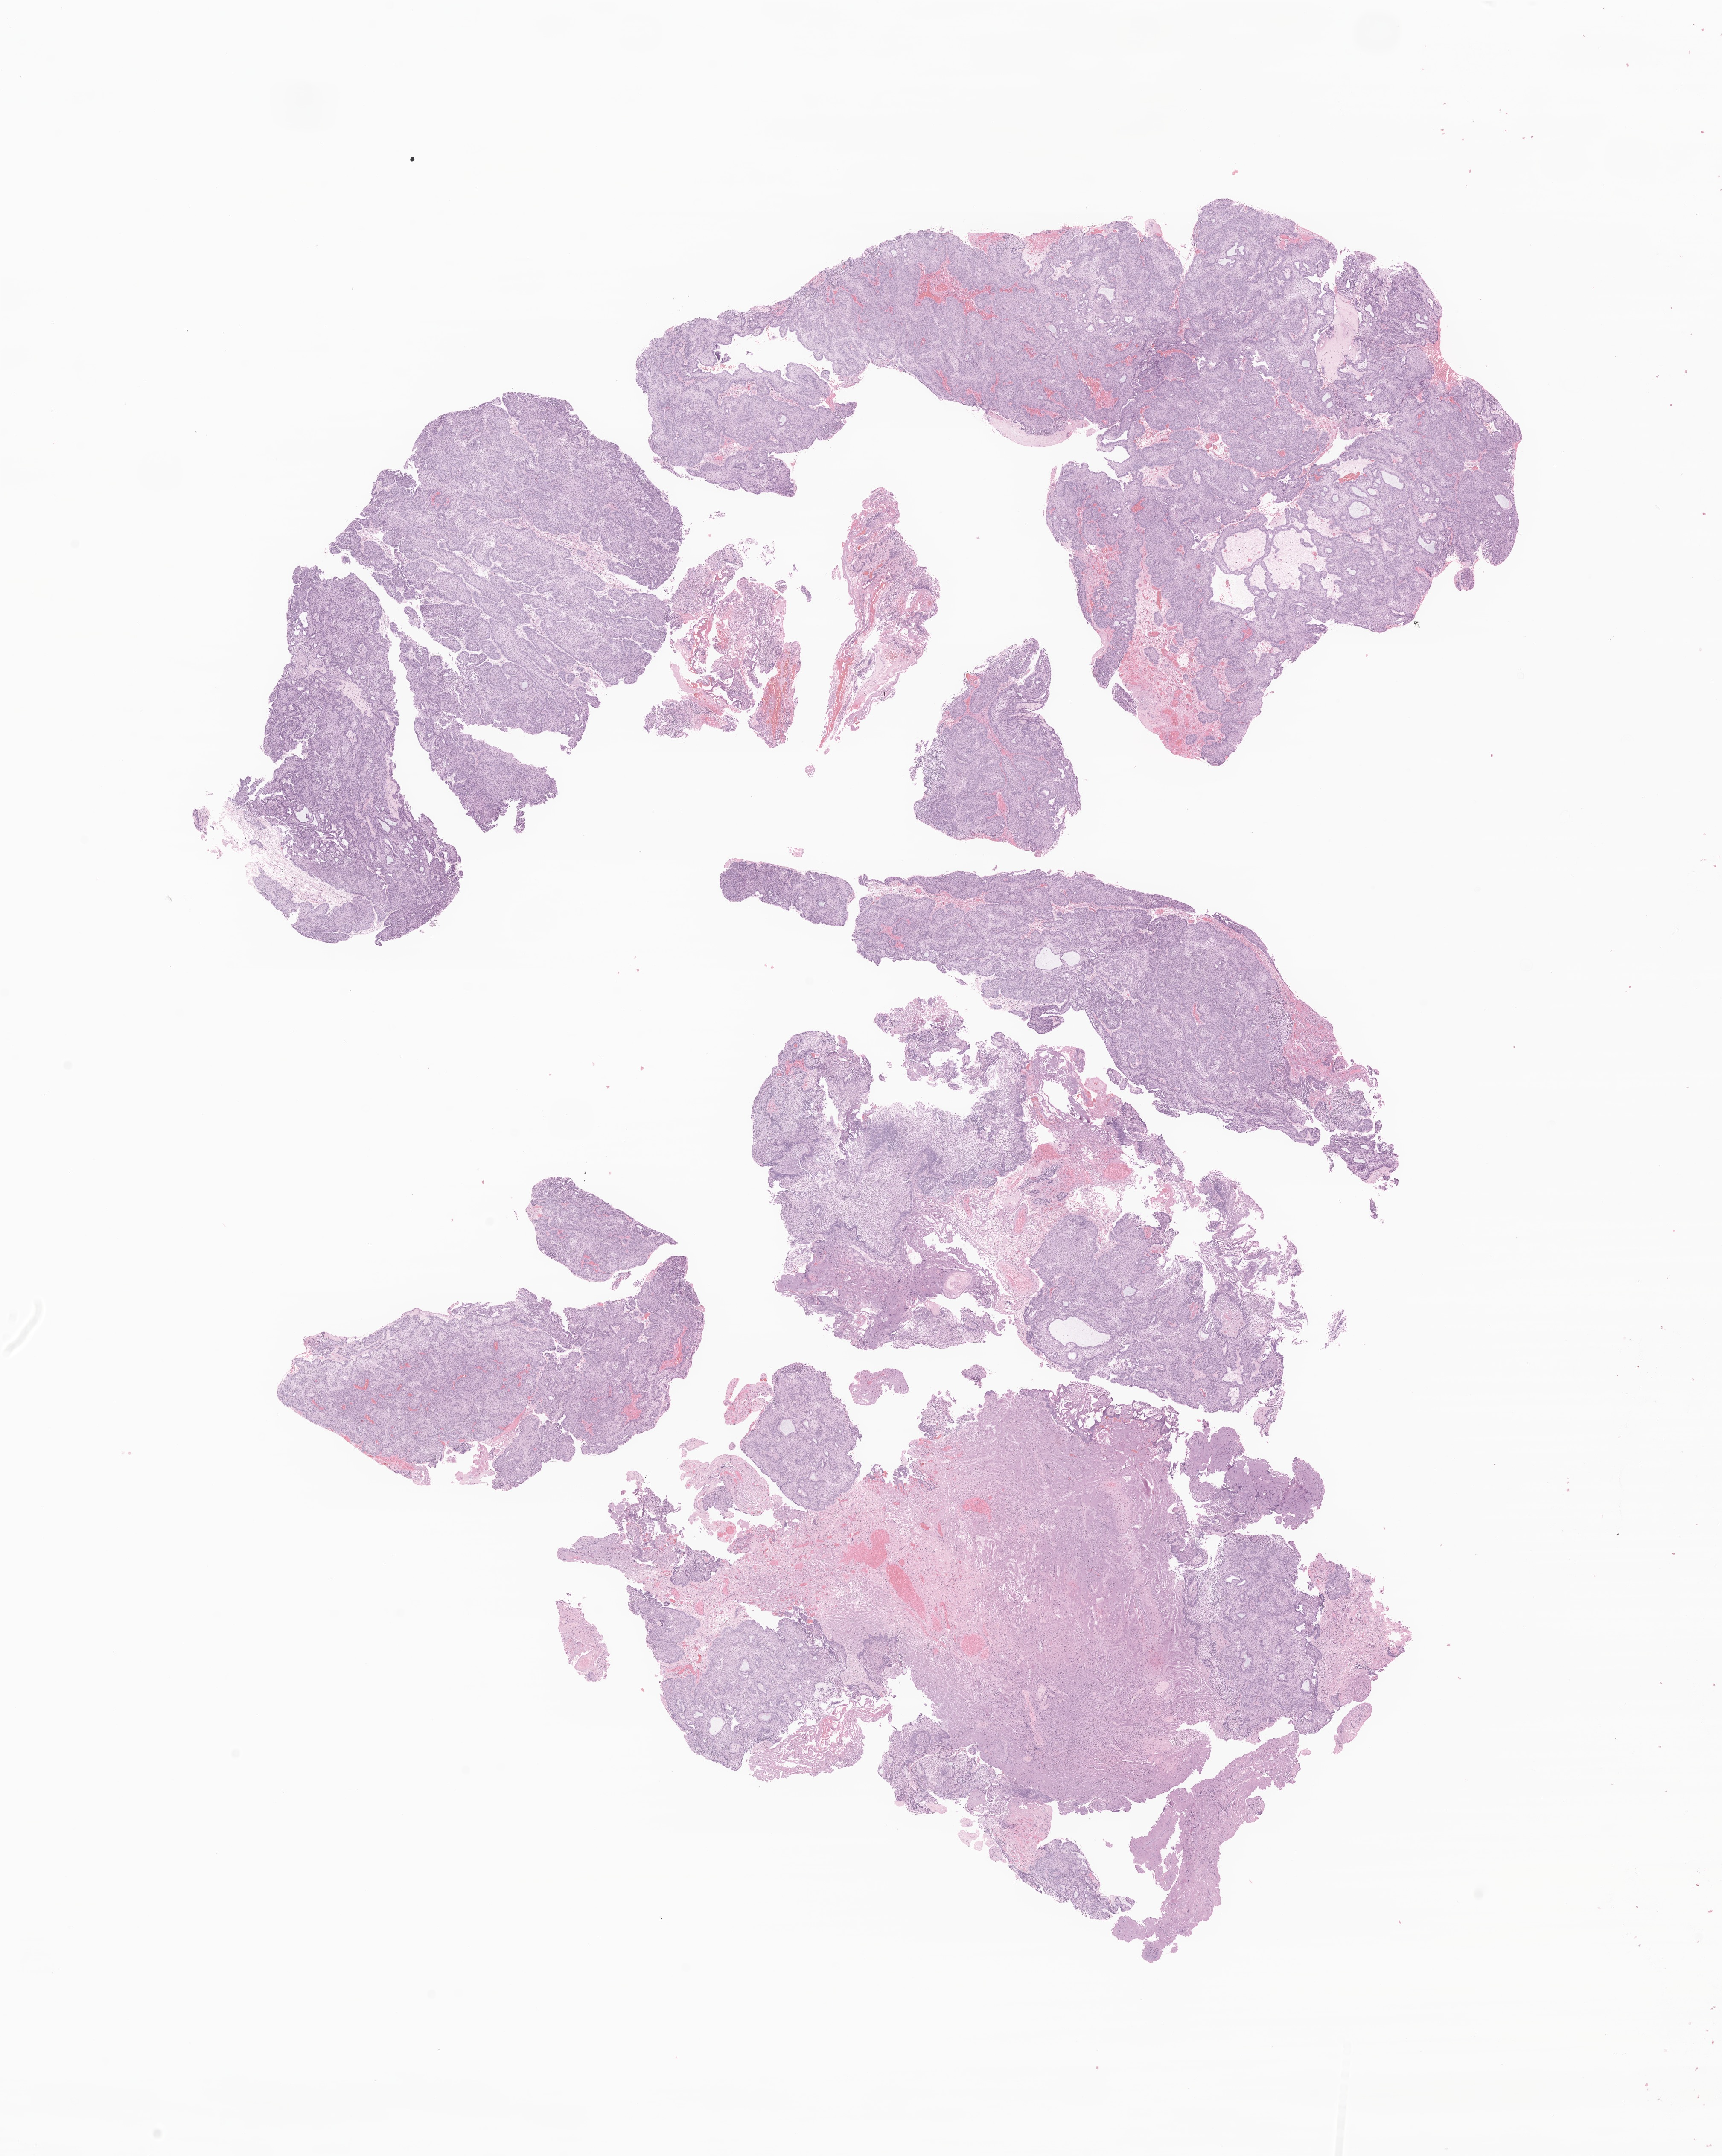
Digitized haematoxylin and eosin-stained section of tumor tissue from the brain — shown as a low-resolution overview of the whole scanned area (about 17.0 x 21.3 mm), formalin-fixed paraffin-embedded section. Patient: female, age 57 months.
Recorded diagnosis: Craniopharyngioma, adamantinomatous.